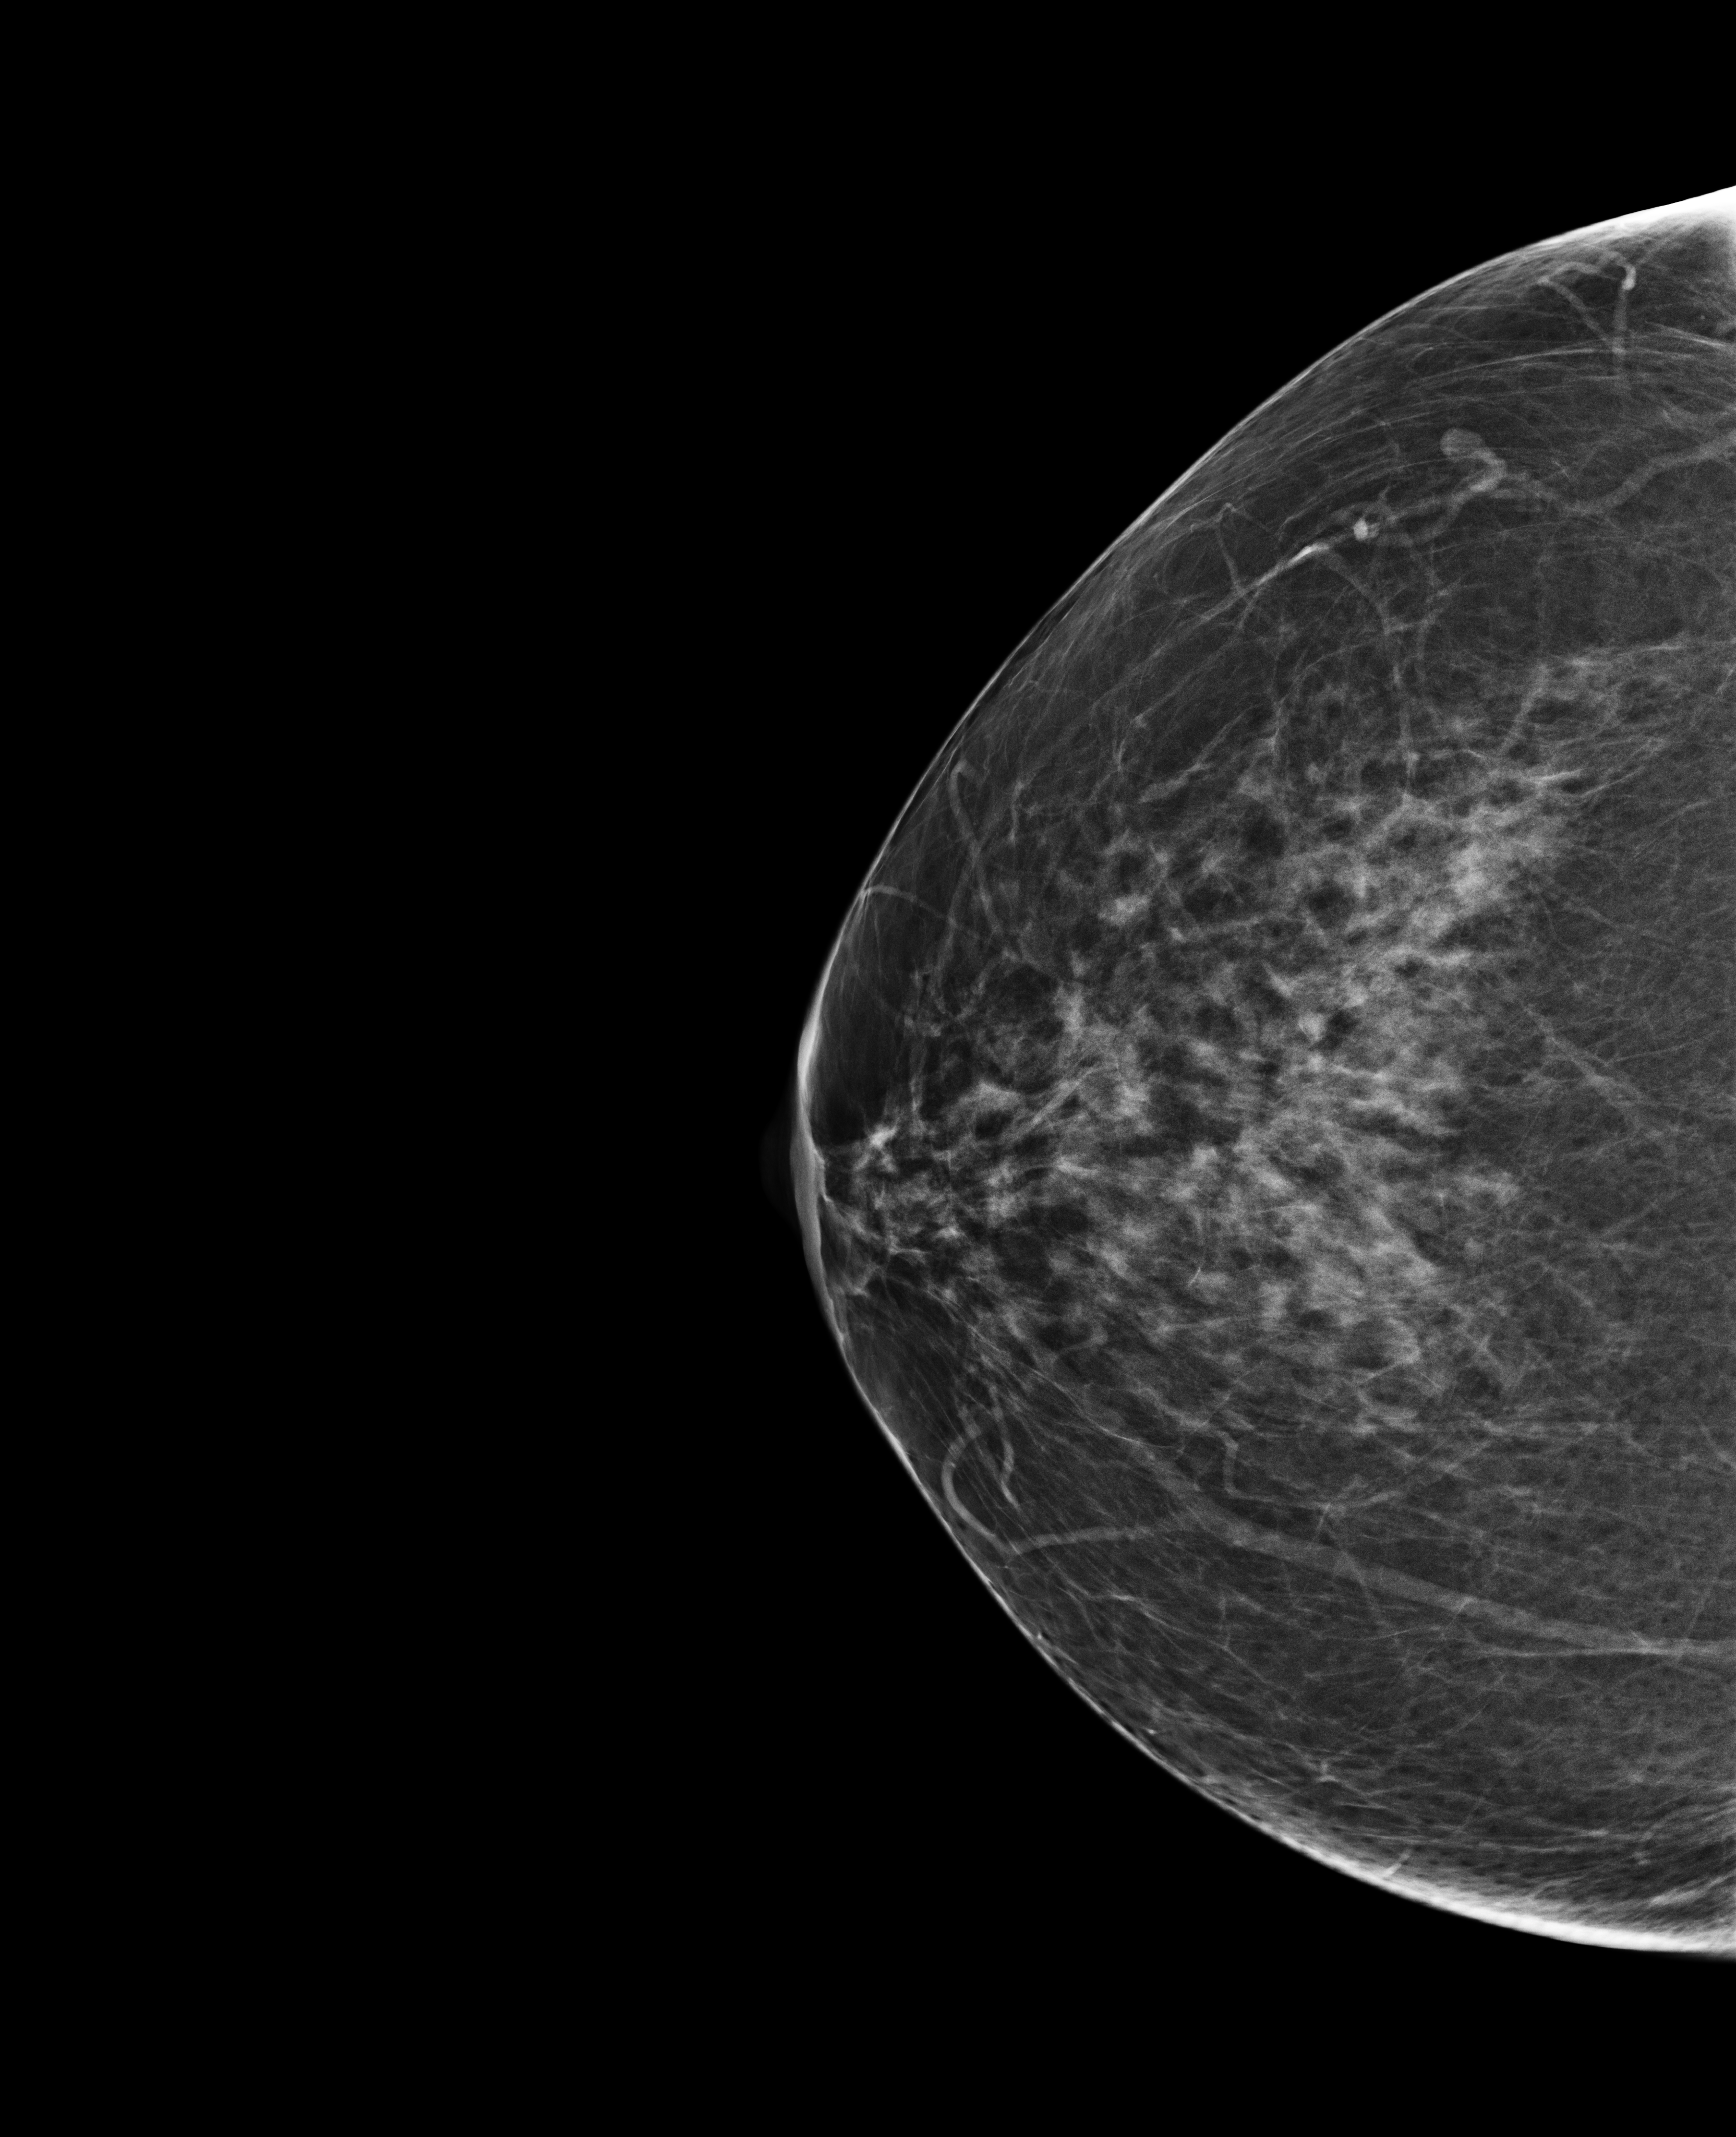
Annual screening mammography examination, compressed breast thickness 77 mm, system: Selenia Dimensions. Patient aged 60 years (female).
Image type: full-field digital mammogram. Breast: right. Projection: cranio-caudal projection.